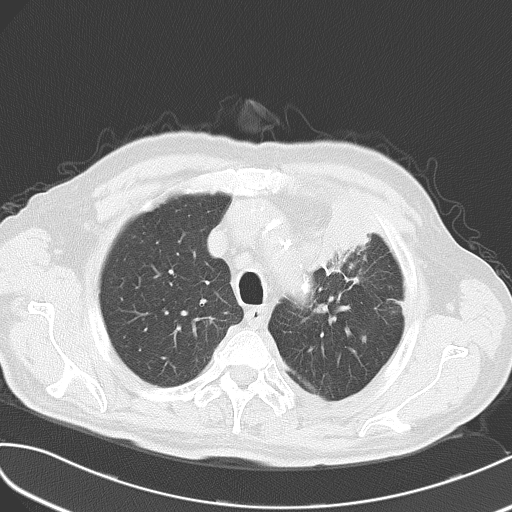
Chest CT, one axial slice. Slice 44 of 54 in the series (ordered by position). Reconstruction kernel B70f. Lung window (W 1500 / L -600 HU). 5 mm slice thickness. 512 × 512 image matrix. Male patient, age 70 years. From the clinical record (not read from this slice): clinical TNM (as recorded): T2 N1 M3; histopathological grade: G3.
Annotated regions visible in this slice (rectangle marked by the reading radiologist):
- lung tumour (recorded histology: small cell carcinoma): bounding box (x1, y1, x2, y2) in pixels: (307, 182, 384, 286)